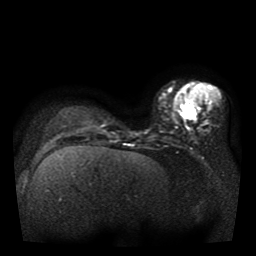
Breast MRI, one axial slice. Slice 15 of 41 in the series (ordered by position). Diffusion-weighted series; image 2 of 4 stored at this slice position (different b-values; order by instance number). 1.5 T. 5 mm slice thickness. 256 × 256 image matrix, field of view 330 × 330 mm. Female patient.
Outlined on this slice (manually delineated by an expert):
- tumour on diffusion-weighted imaging: bounding box [x1, y1, x2, y2] px = [183, 106, 196, 120]